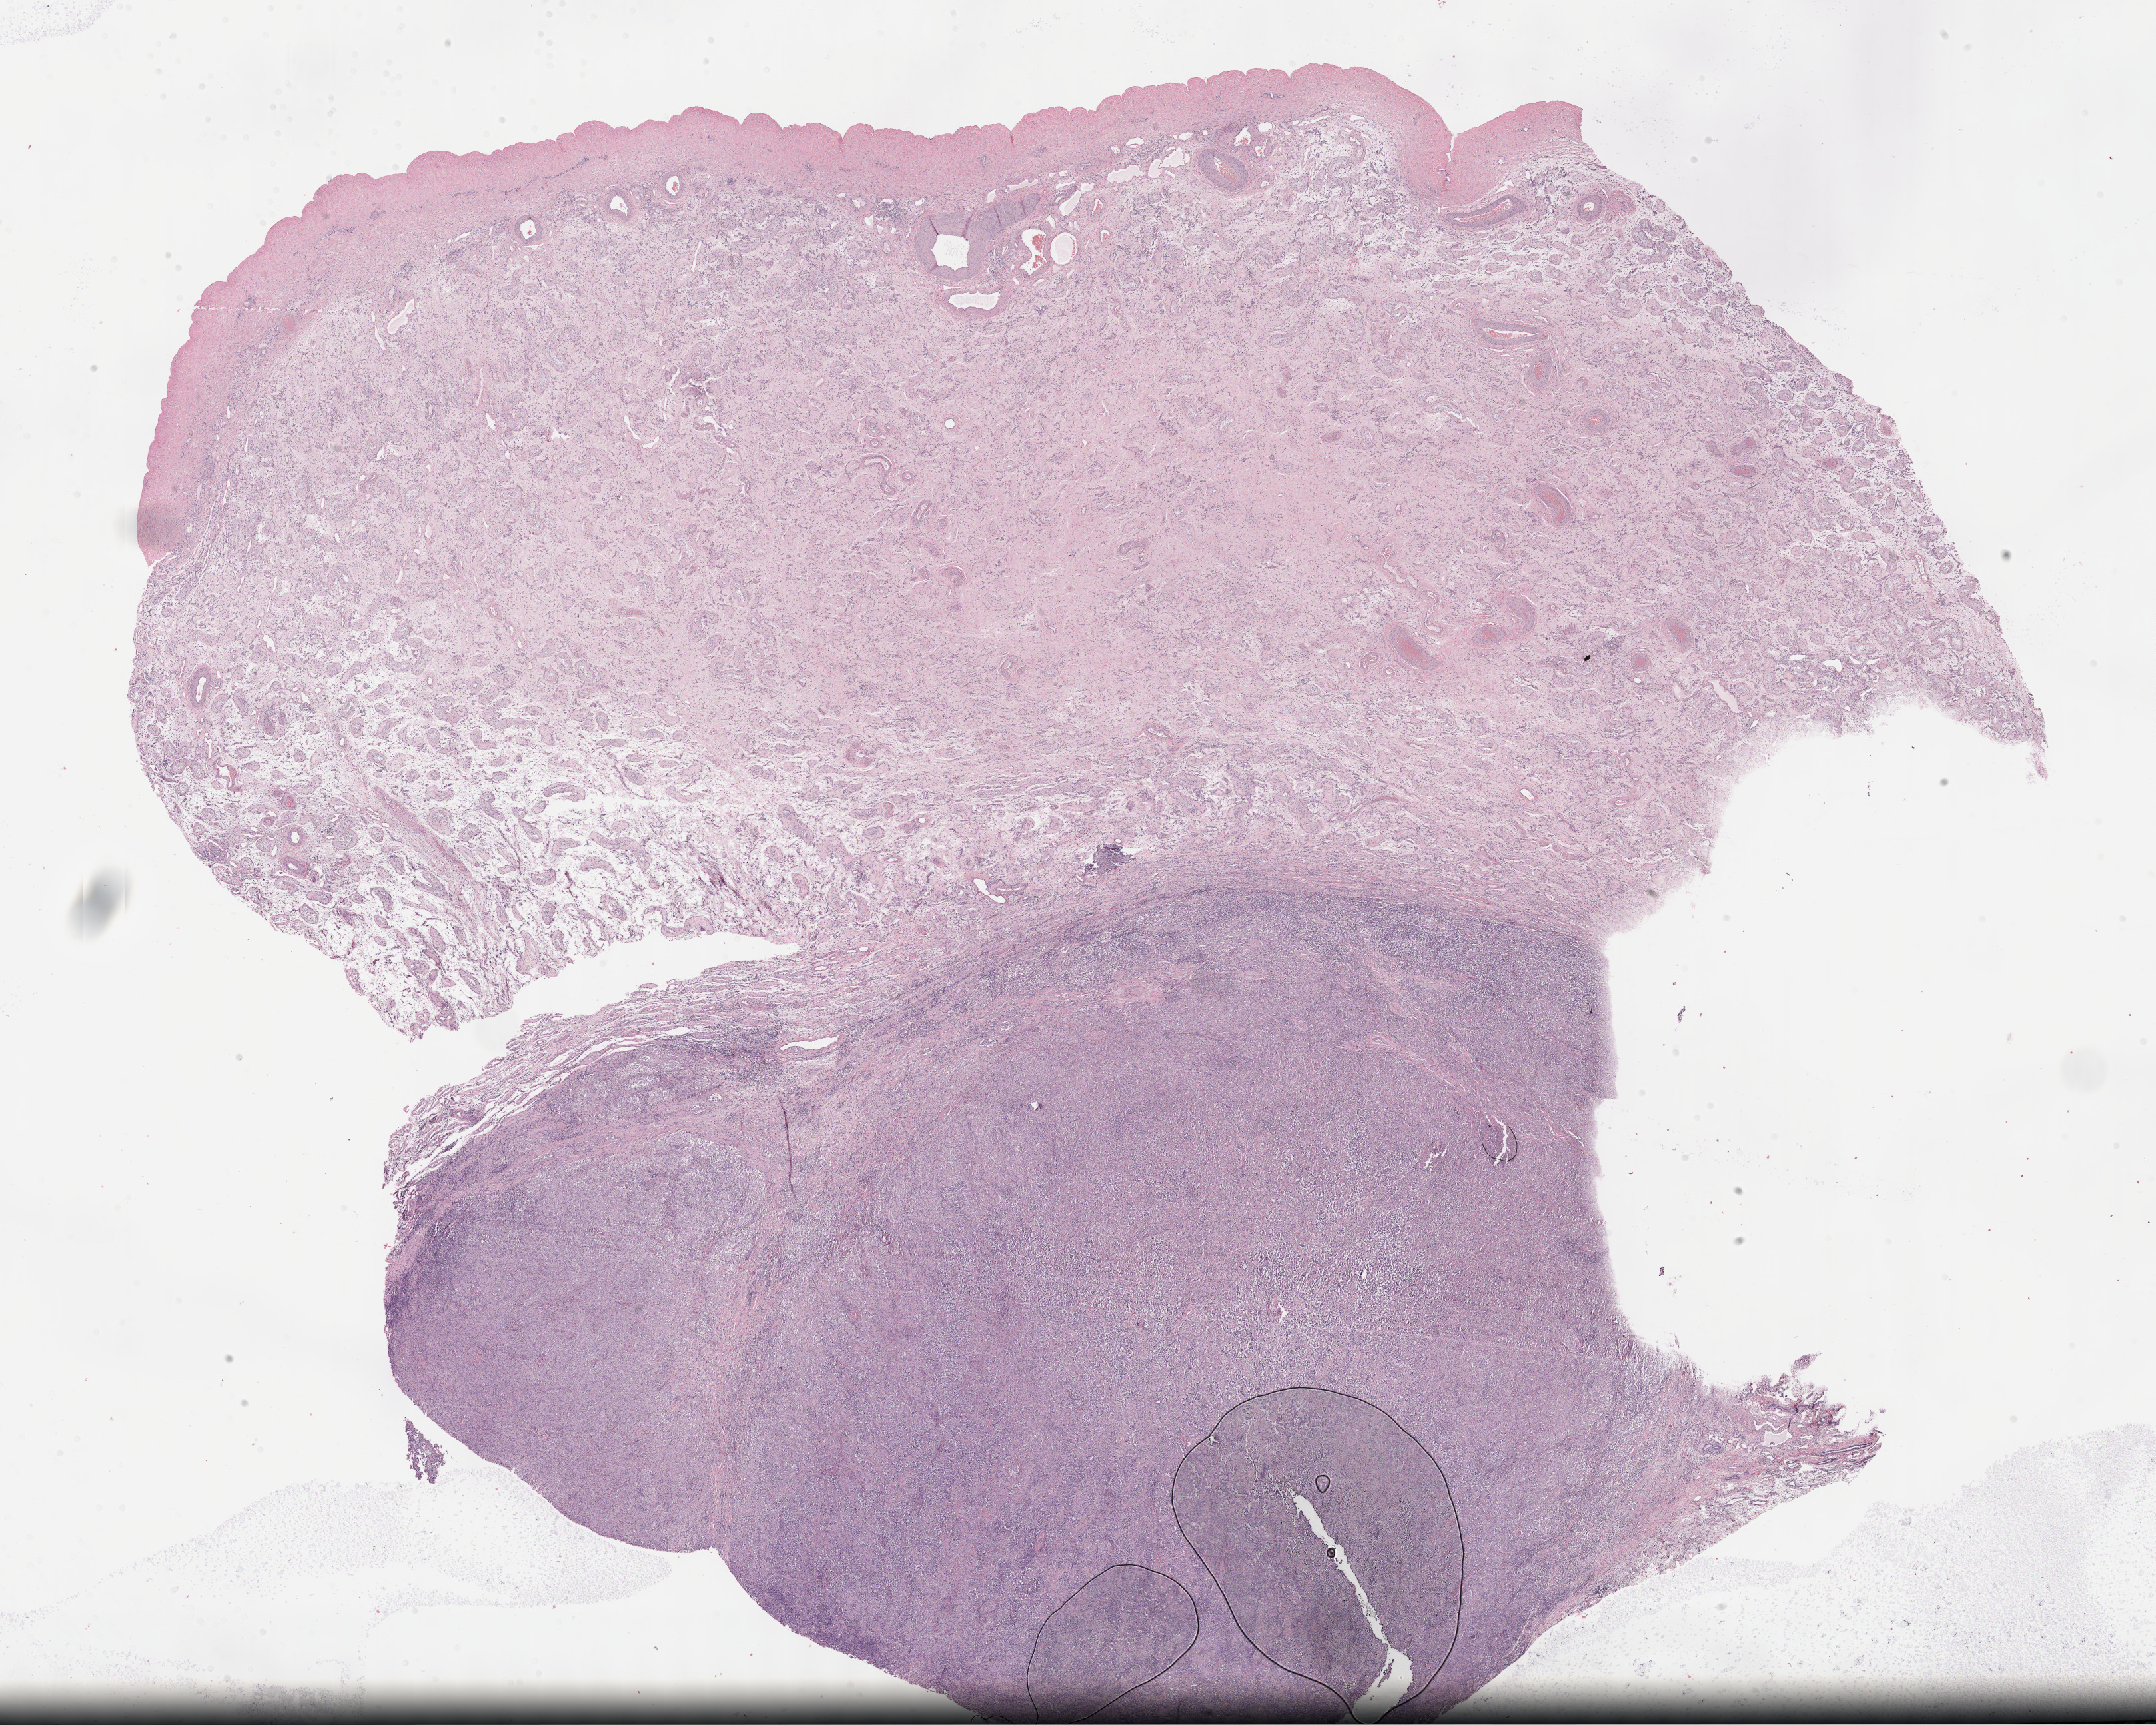
H&E whole-slide image — low-resolution overview of the scanned area, about 26.2 x 20.9 mm (acquisition: 40x scan), FFPE section, primary tumour sample from the testis. Male patient; age at initial diagnosis 31 years.
TNM: T1 N0 M0. AJCC pathologic stage: IA (7th edition). Histologic diagnosis: Seminoma, NOS.